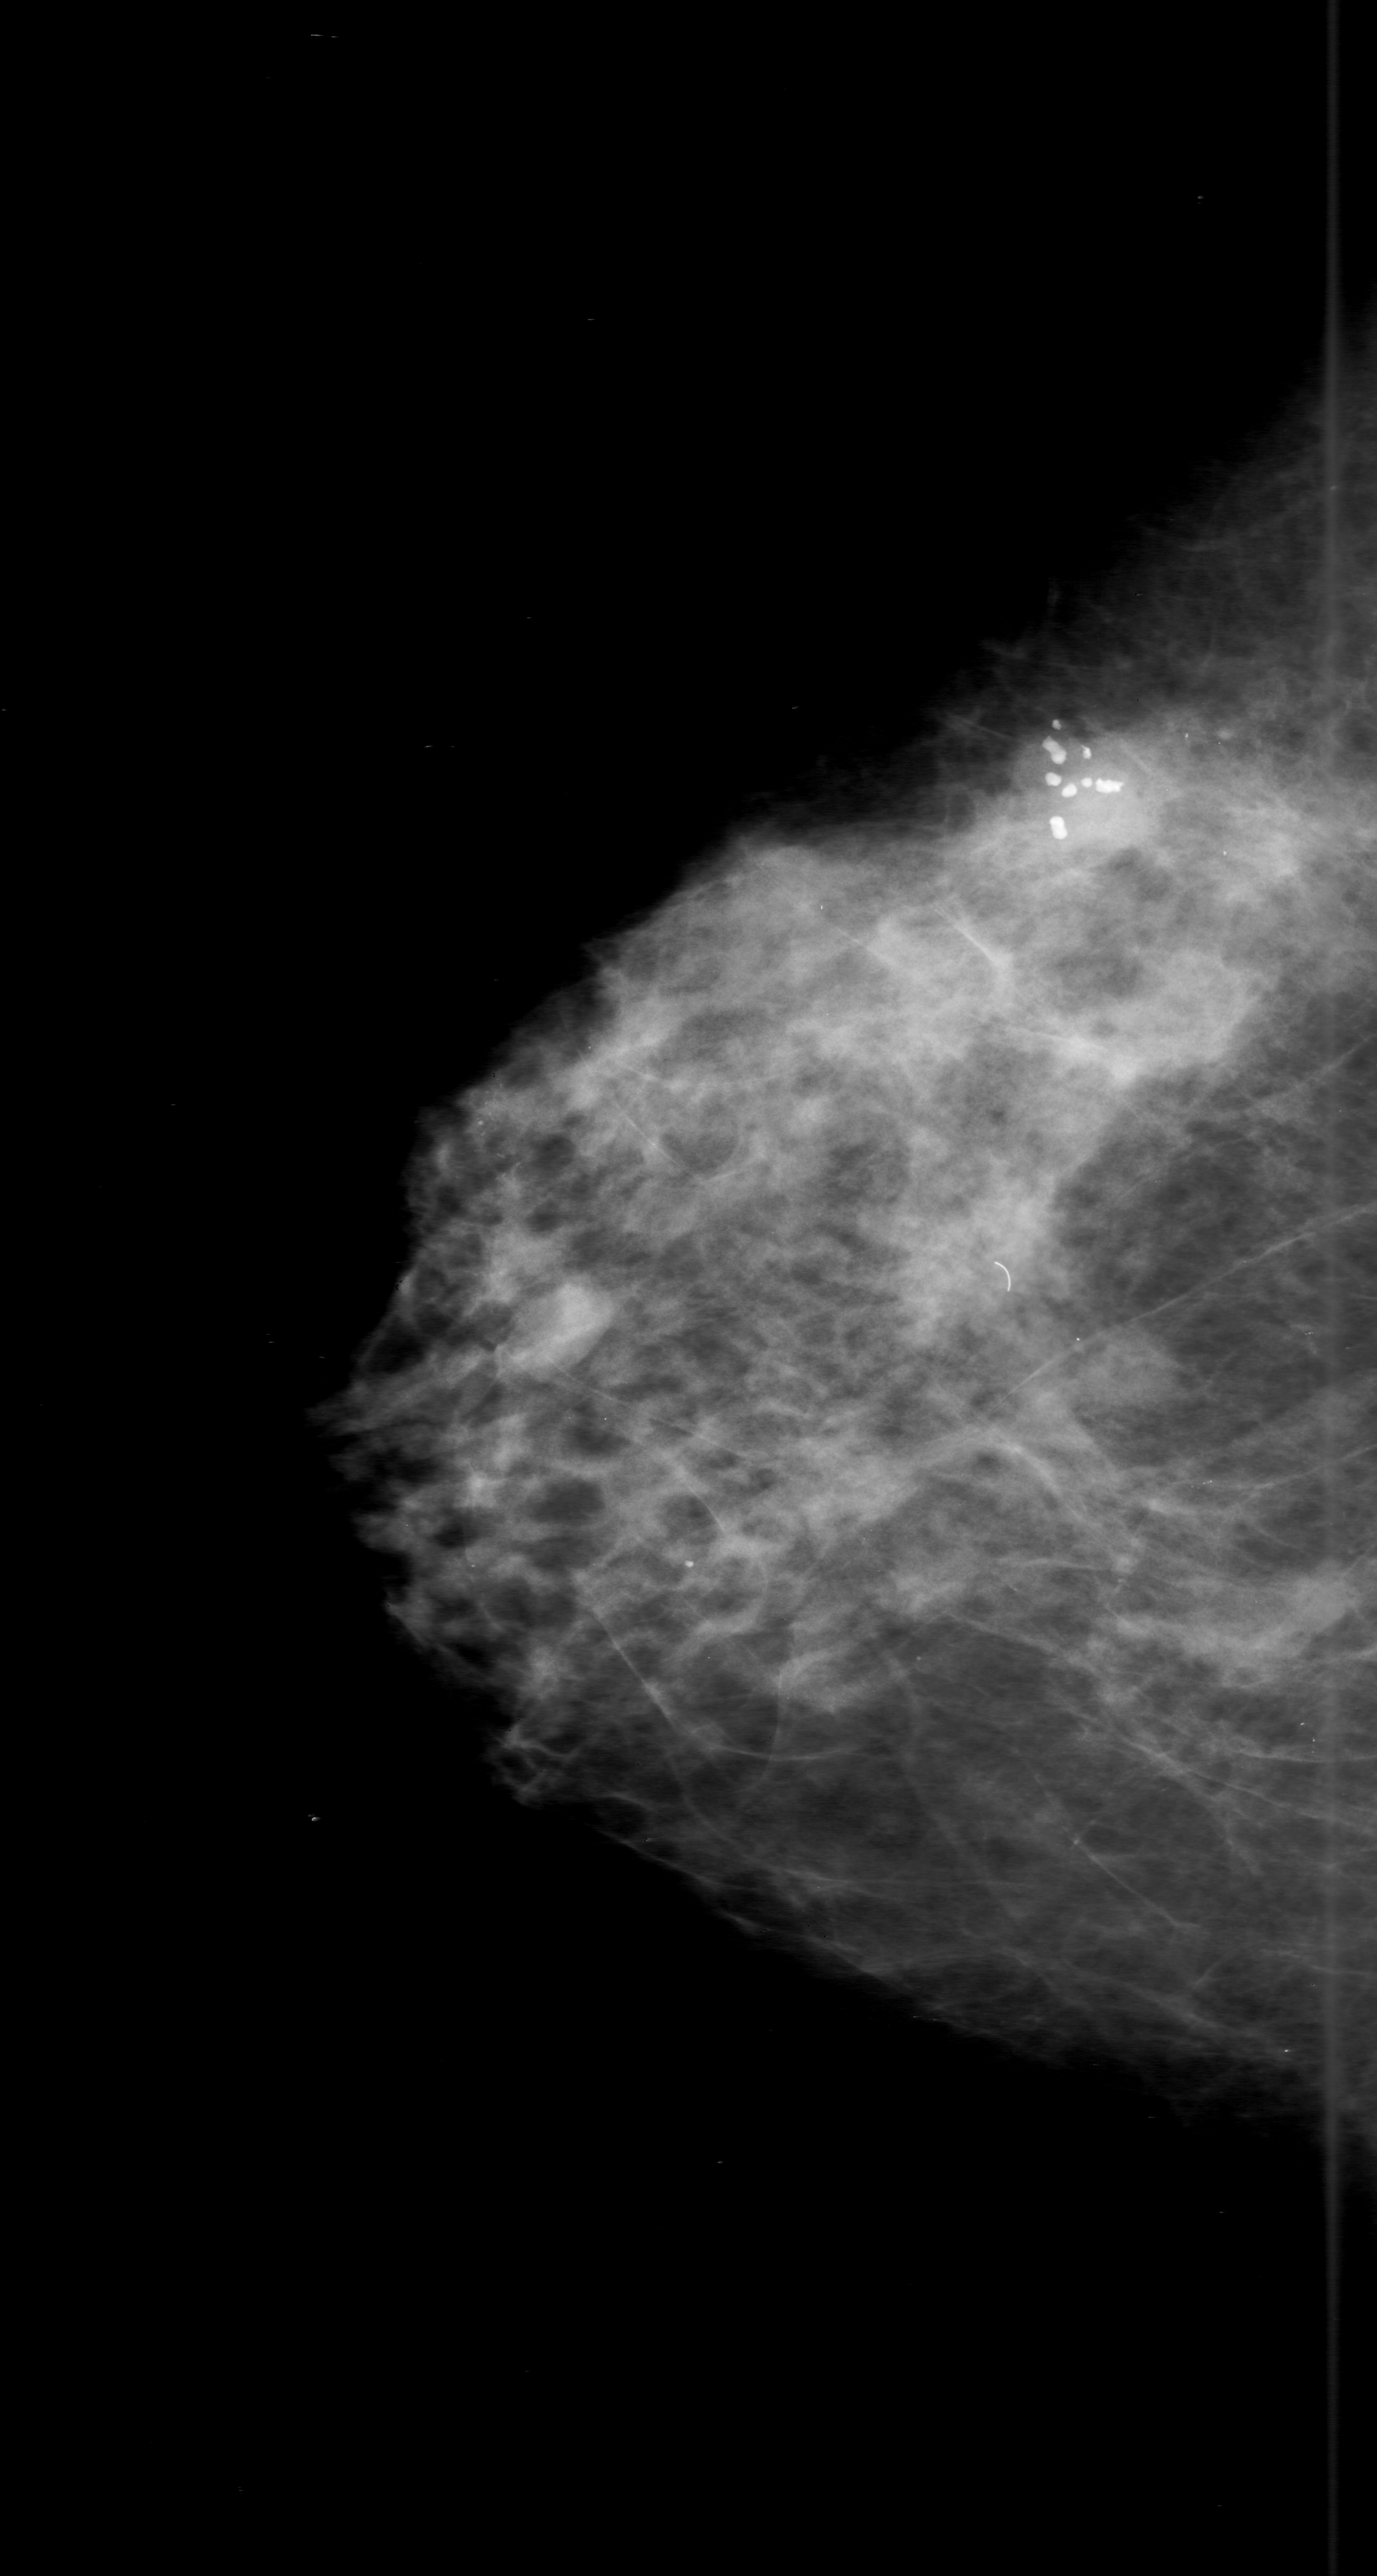
Mammogram (digitized film), right breast, craniocaudal (CC) view, BI-RADS breast density category 3 (scale 1–4).
Finding: calcifications, morphology punctate / fine linear branching, distribution clustered; BI-RADS assessment category 0 (incomplete: needs additional imaging); pathology result (as recorded, not read from the image): malignant.